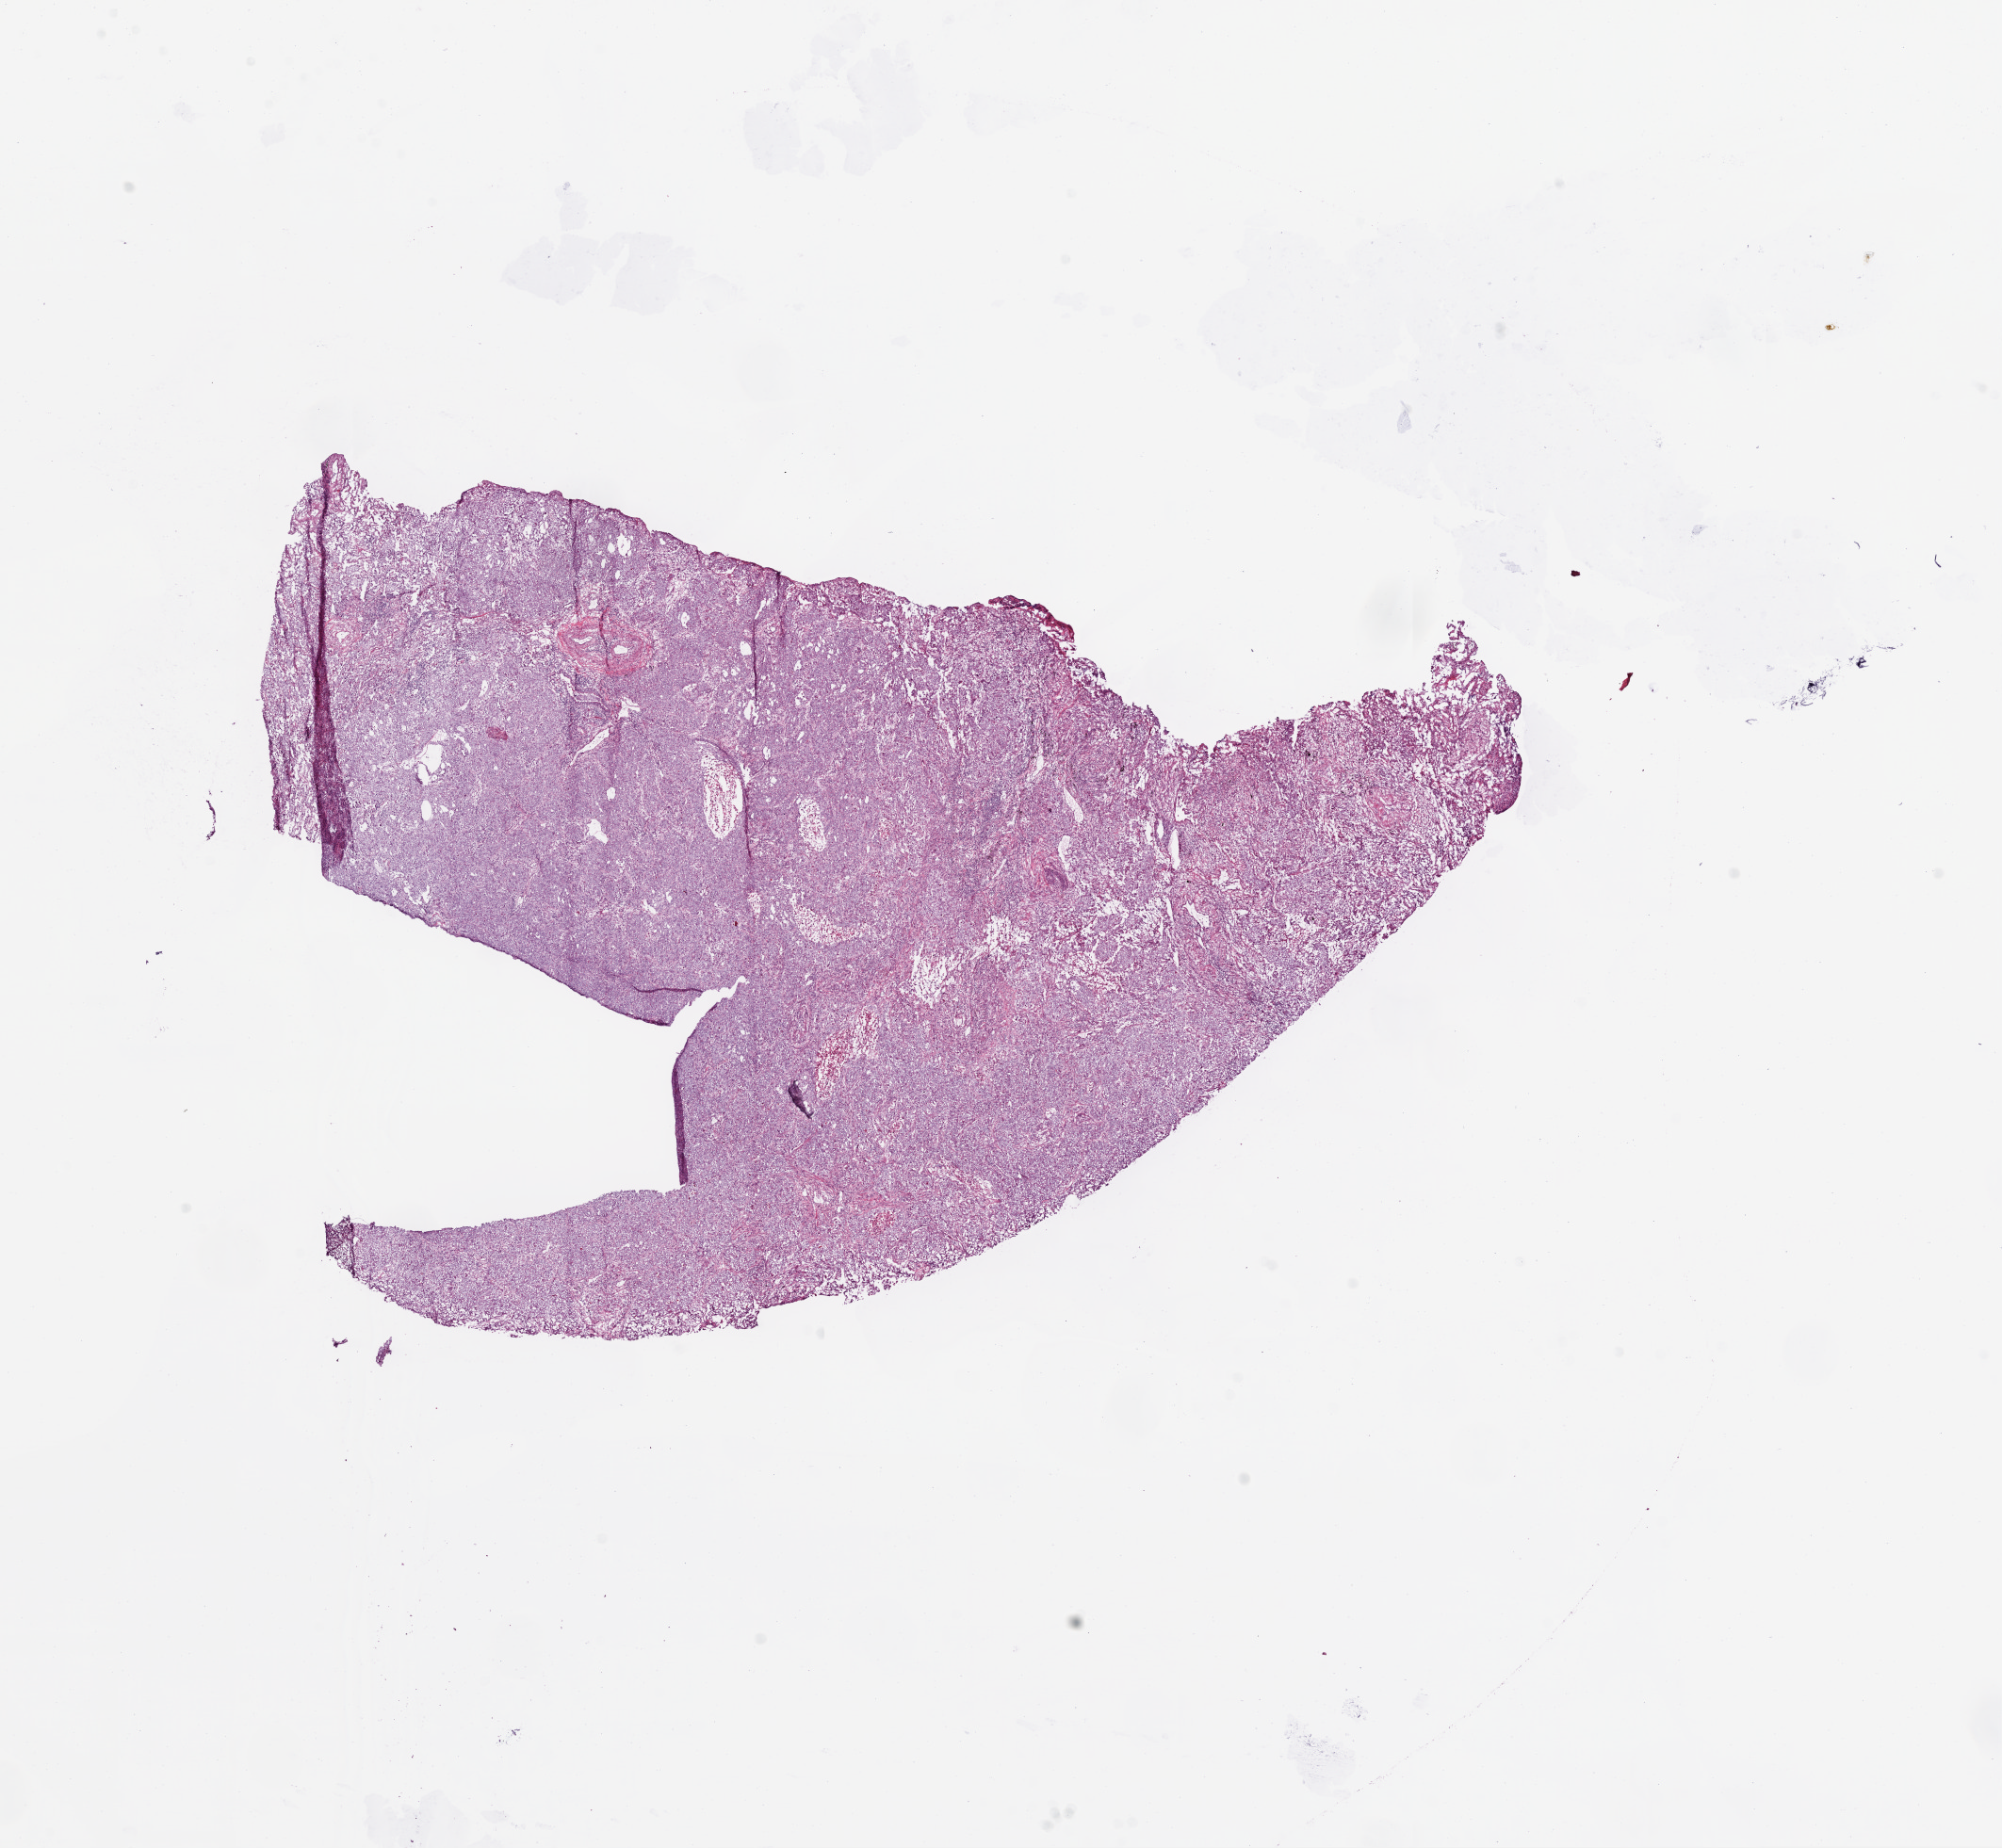
Digitized Hematoxylin and eosin (H&E) stained tissue section (whole slide) — shown as a low-resolution overview of the whole scanned area (about 17.1 x 15.7 mm, slide scanned at 20x), frozen section from the bottom of the tissue portion, sample: primary tumour, lung. Female patient; age at initial diagnosis 79 years. Slide review estimates, as recorded: tumour cells 87%, tumour nuclei 85%, normal cells 5%, stromal cells 5%, necrosis 3%.
AJCC pathologic stage: IIIA. Histologic diagnosis: Adenocarcinoma, NOS (lower lobe, lung). Laterality: right.